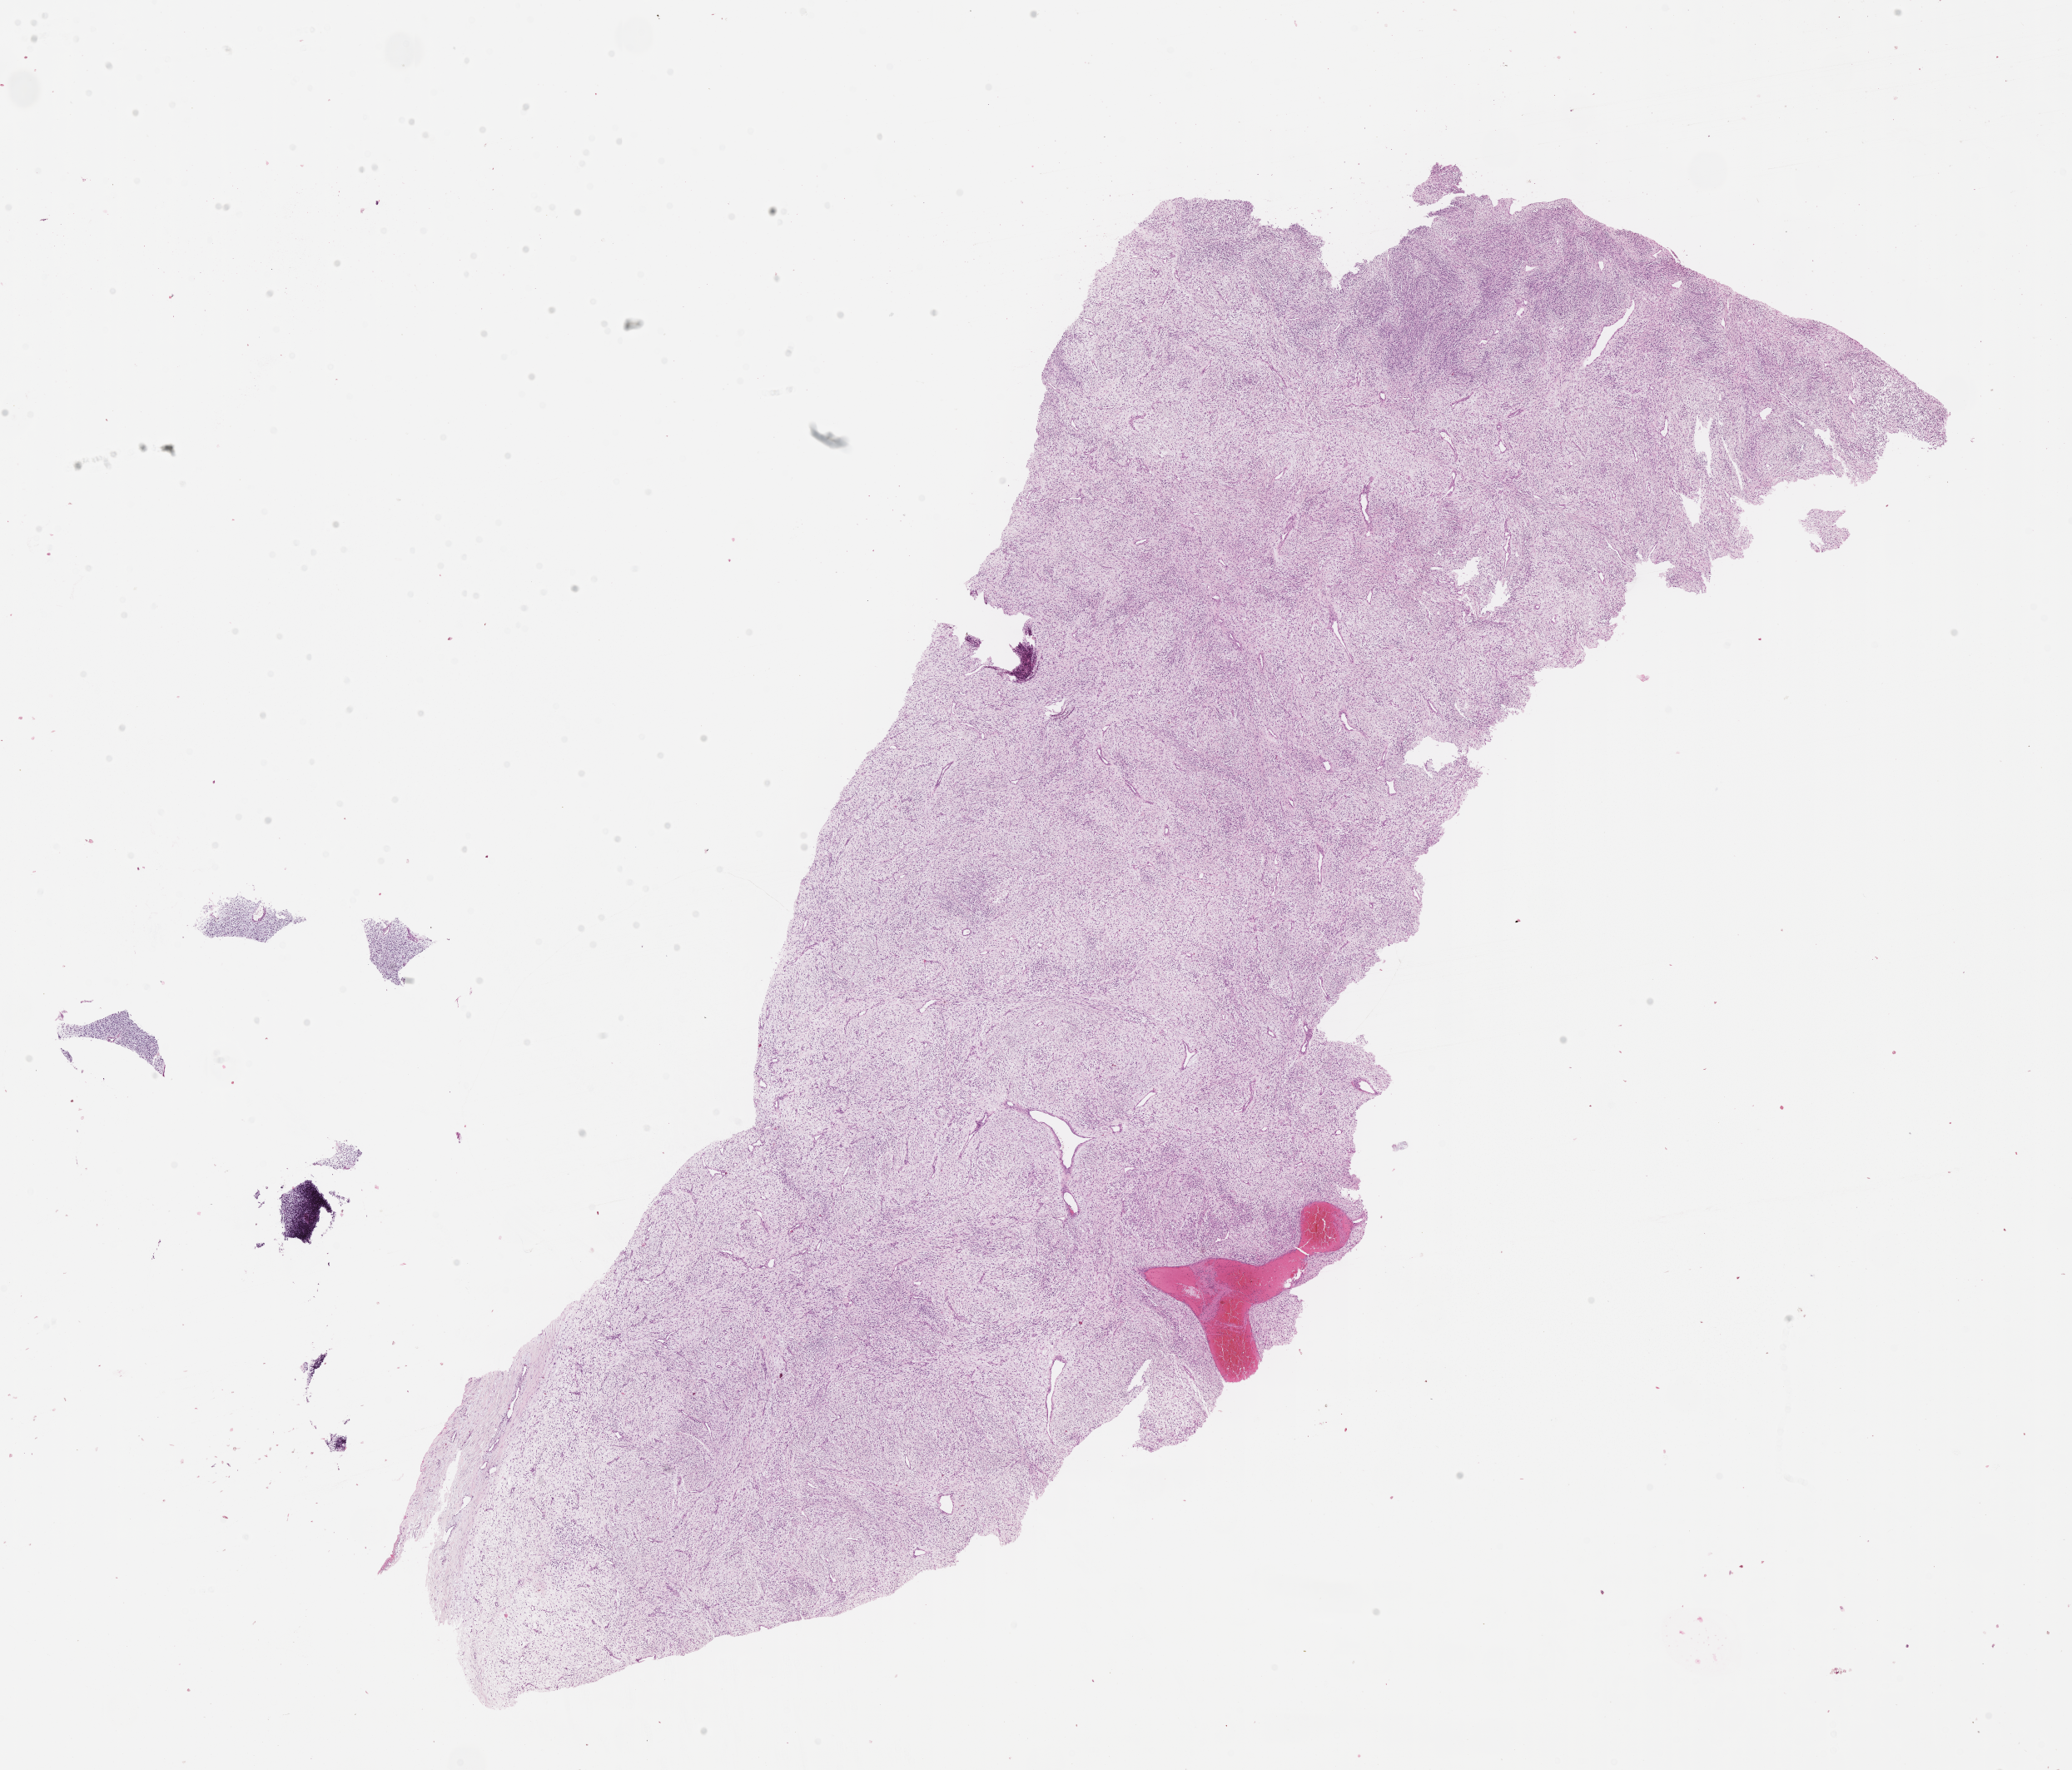
Hematoxylin and eosin (H&E) whole-slide image of tumor tissue — shown as a low-resolution overview of the whole scanned area (about 20.1 x 17.2 mm). Formalin-fixed paraffin-embedded section. Site: retroperitoneum. Patient: male, age 5.5 years at diagnosis.
- diagnosis: rhabdomyosarcoma; histological classification: embryonal rhabdomyosarcoma
- metastatic status at presentation (as recorded): metastatic (confirmed)
- stage (as recorded): 4